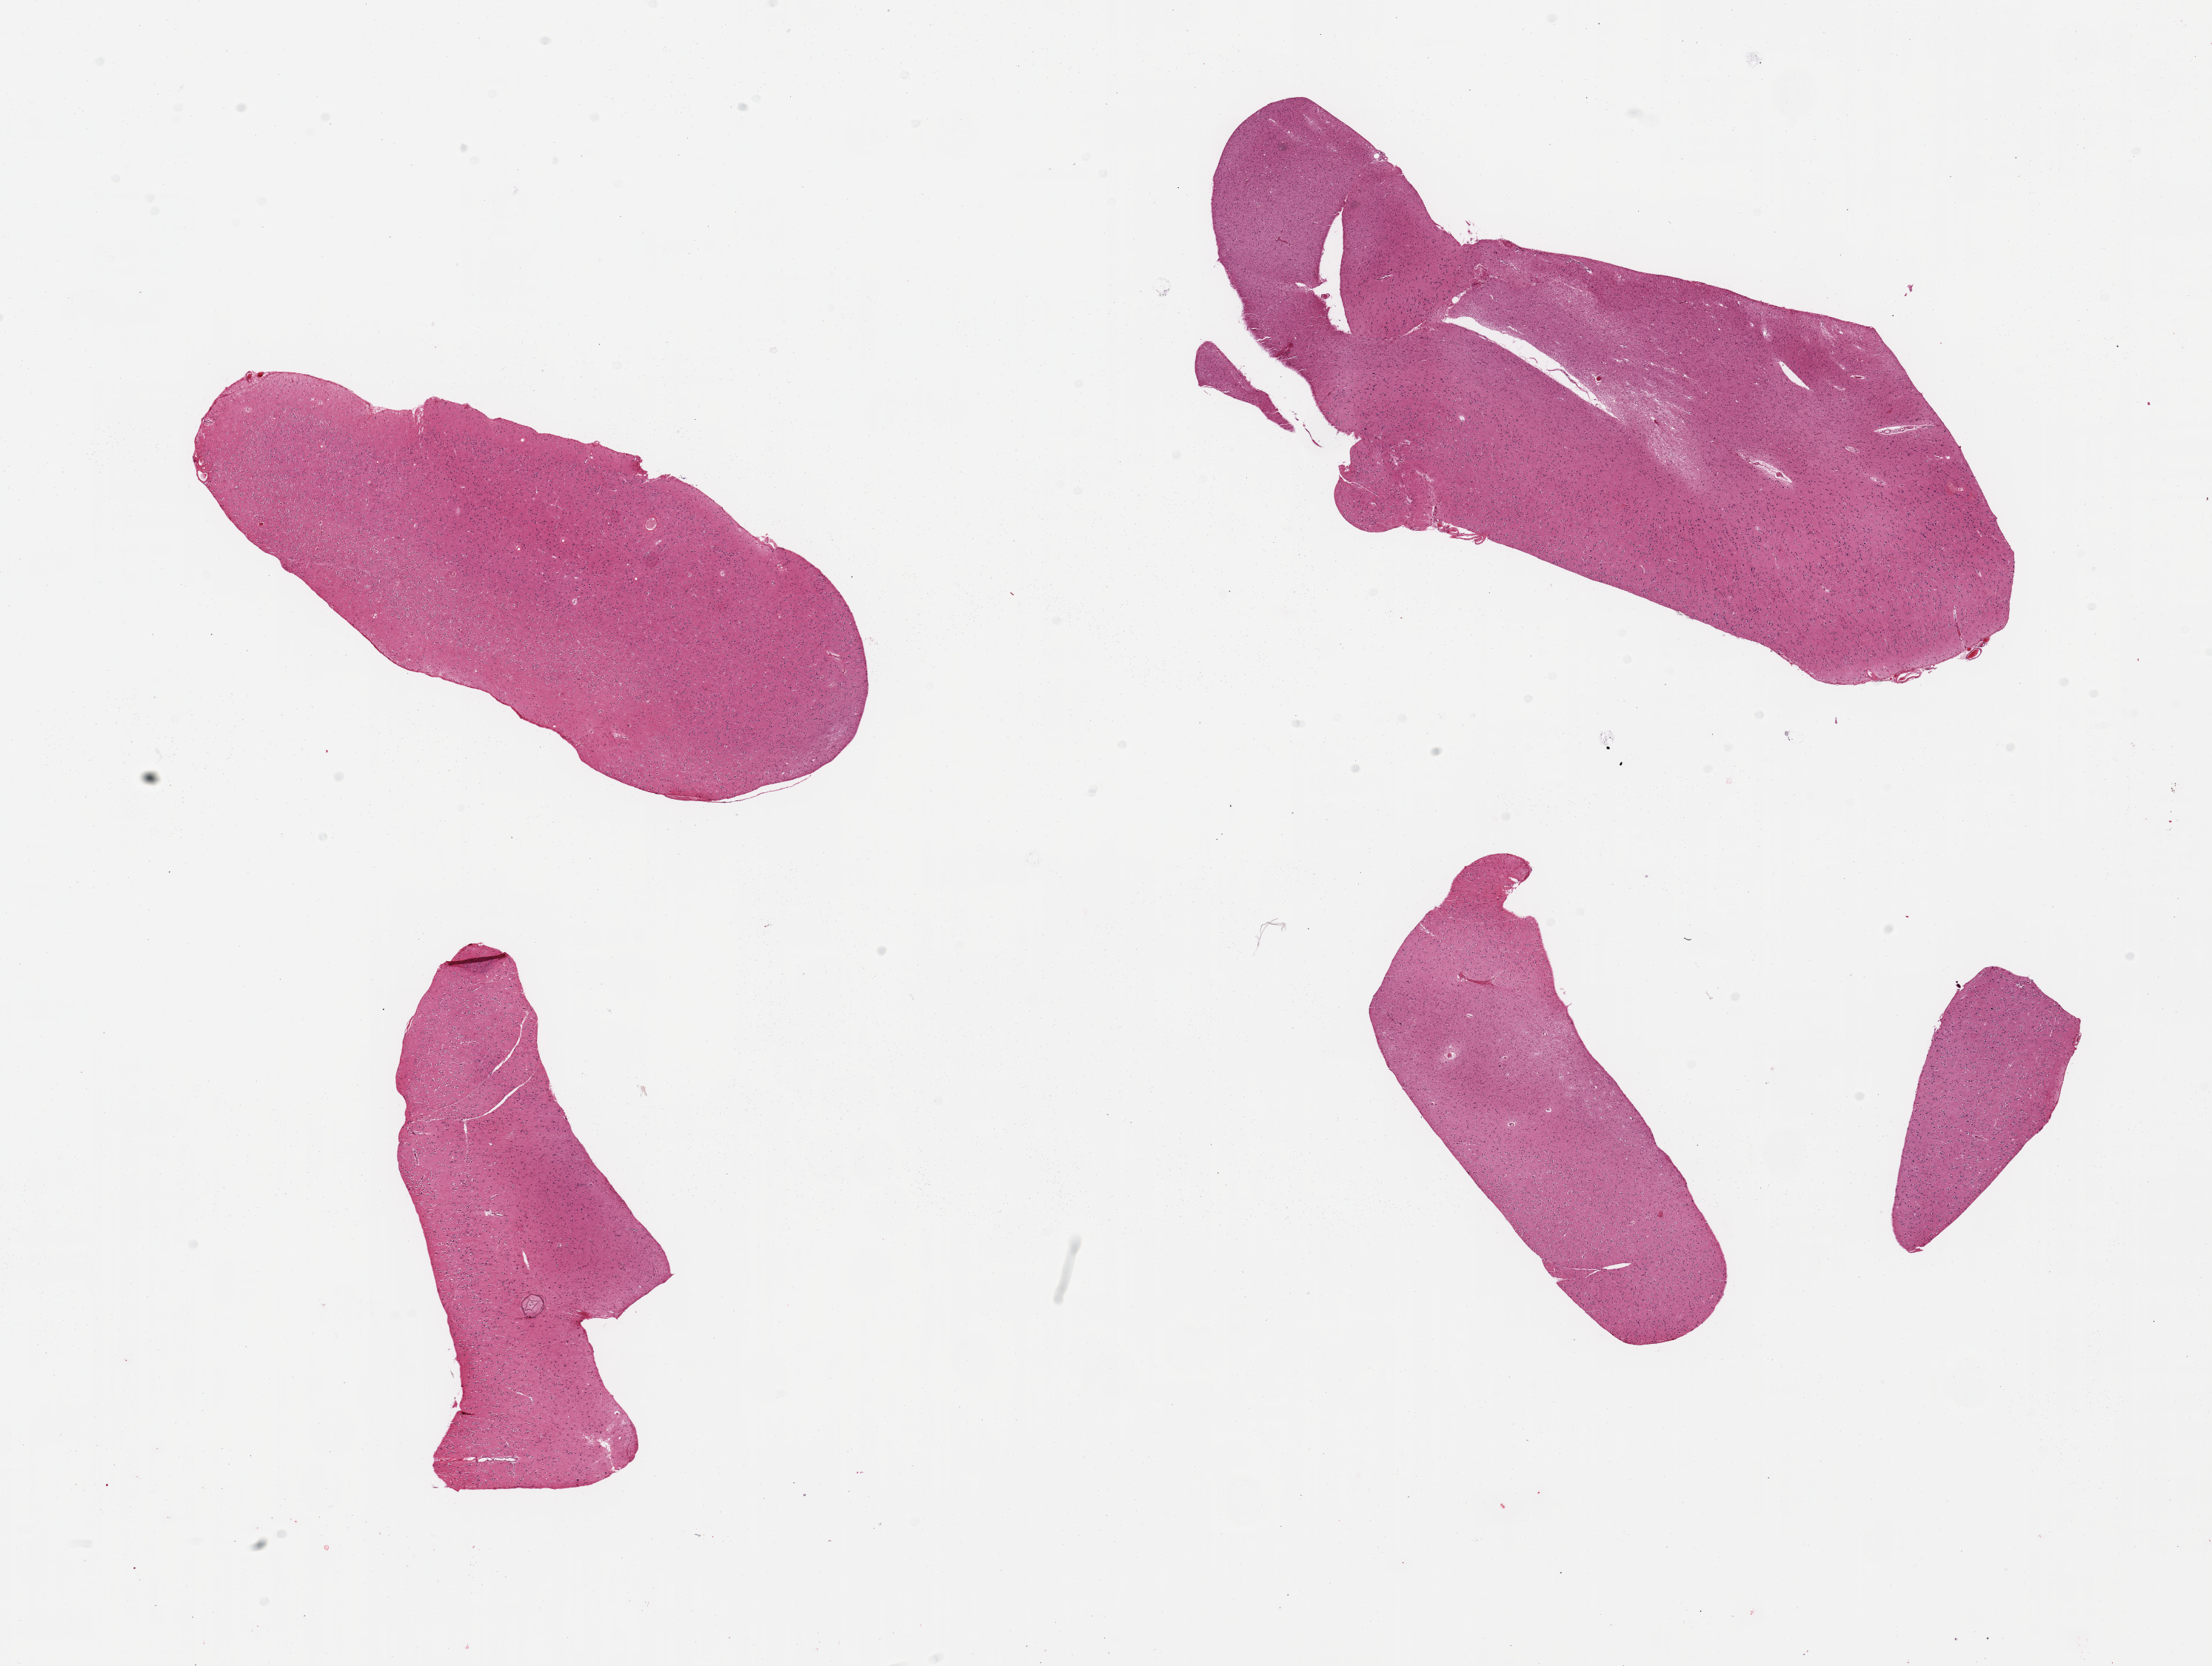
Digitized haematoxylin and eosin-stained section, low-resolution overview of the scanned area, about 23.6 x 17.8 mm (slide scanned at 20x), PAXgene-fixed paraffin-embedded (PFPE) section, sampled site (target tissue): cerebral cortex, donor tissue sample. Donor sex: male.
Reviewer comment on this tissue sample: 4 pieces, no abnormalities.